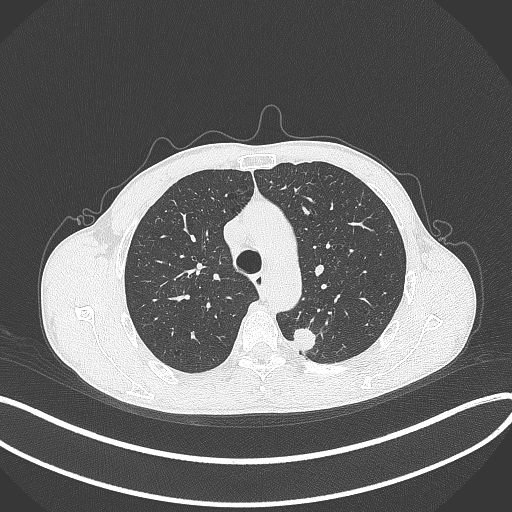
Chest CT, one axial slice. Slice 290 of 429 in the series (ordered by position). Reconstruction kernel B70f. Lung window (W 1500 / L -600 HU). 512 × 512 image matrix, field of view 400 × 400 mm. Male patient, age 51 years. Case-level facts recorded for this patient, not image findings: clinical TNM (as recorded): T2a N1 M1.
Structures marked on this image (bounding box drawn by a radiologist):
- lung tumour (recorded histology: adenocarcinoma): box from (x=290, y=324) to (x=319, y=357) px